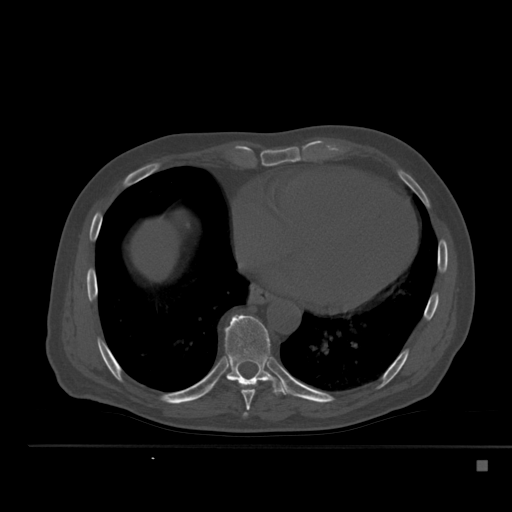
CT including the spine, one axial slice; slice 296 of 517 in the series (ordered by position); reconstruction kernel Br40s; 120 kVp; bone window (W 1800 / L 400 HU); 1.5 mm slice thickness; 512 × 512 image matrix, field of view 408 × 408 mm. Male patient, age 70 years. Case-level facts recorded for this patient, not image findings: primary cancer: renal; vertebrae with lytic lesions (as recorded): T4, T6, T10, T12, L3, L4, L5.
Structures marked on this image (semi-automatic segmentation, software-assisted and operator-edited):
- T7 vertebra: bounding box <244,413,247,416> (left, top, right, bottom; pixels)
- T8 vertebra: <239,380,260,410>
- T9 vertebra: <212,314,286,396>